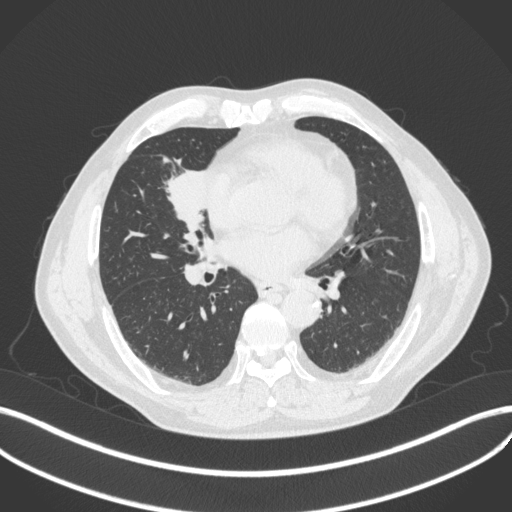
Chest CT, one axial slice. Position 187 of 429 along the scan axis. 120 kVp. Lung window (W 1500 / L -600 HU). 1 mm slice thickness. 512 × 512 image matrix, field of view 400 × 400 mm. Patient: male, 61 years. Case-level facts recorded for this patient, not image findings: clinical TNM (as recorded): T2b N1 M0.
Structures marked on this image (rectangle marked by the reading radiologist):
- lung tumour (recorded histology: squamous cell carcinoma): bounding box [x1, y1, x2, y2] px = [161, 164, 215, 226]